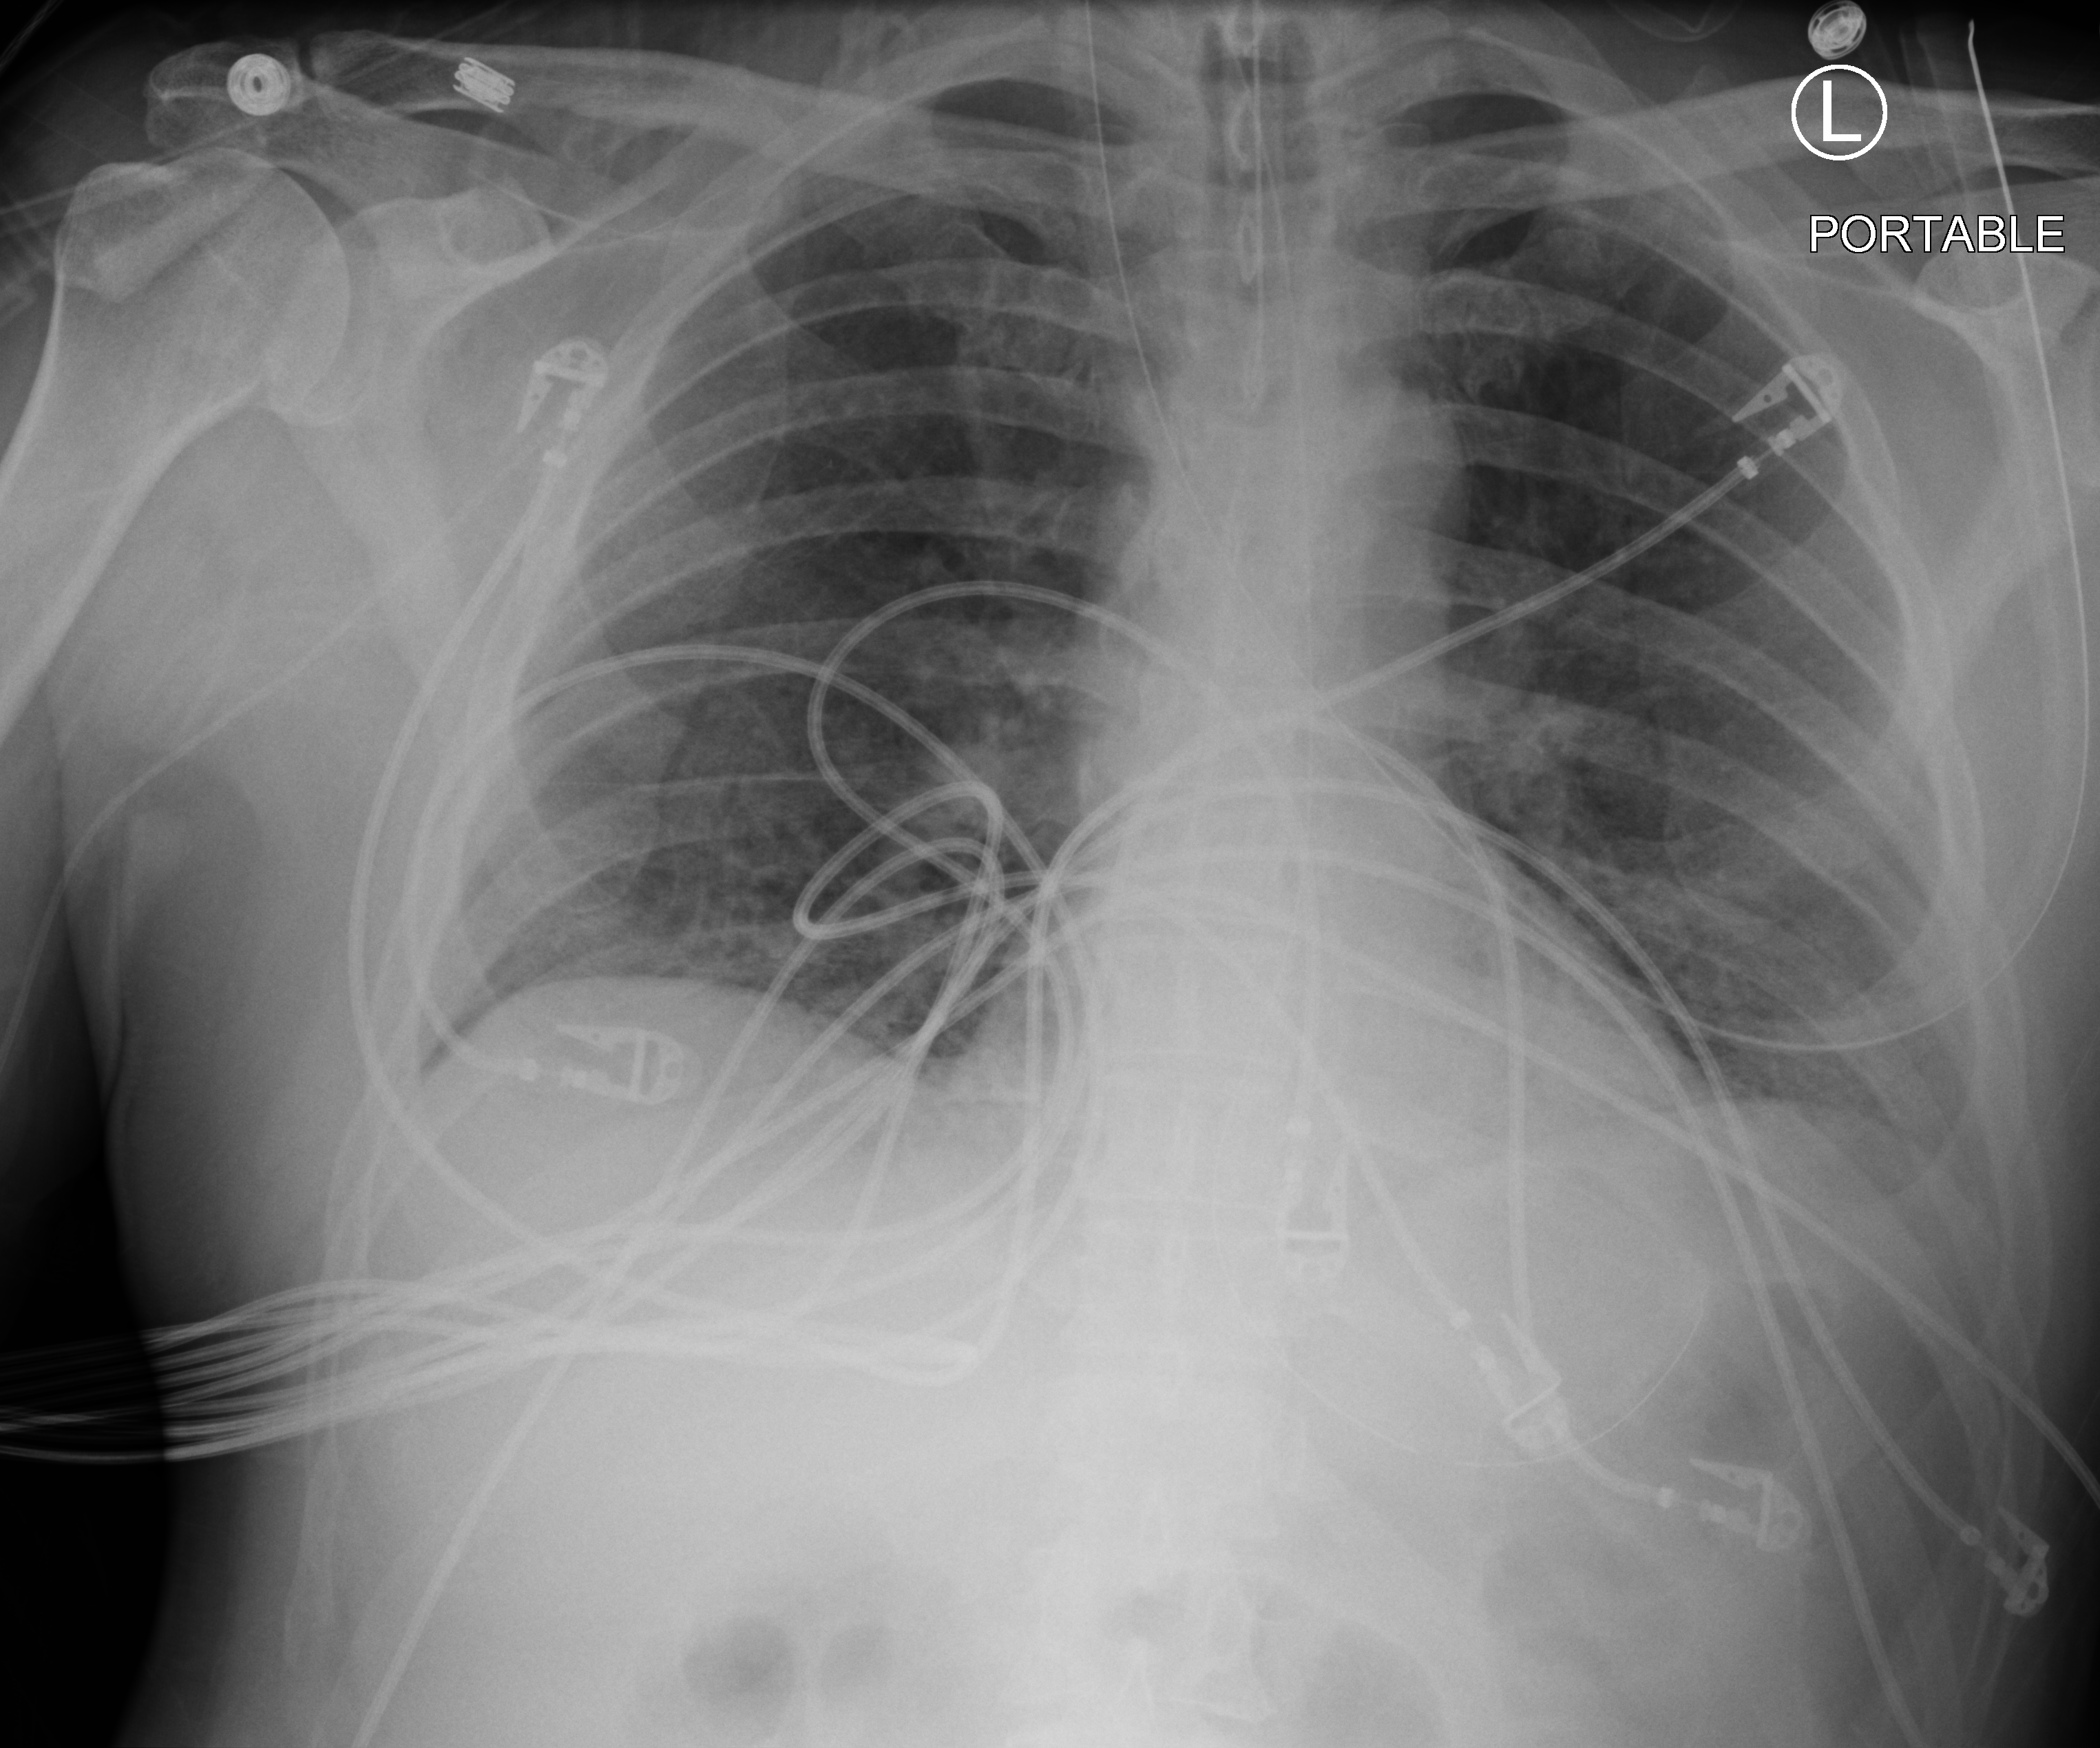
Chest X-ray (portable); anteroposterior (AP) projection. Male patient hospitalised with COVID-19, age 60–74 years.
Hospital-stay facts (about this admission, not read from this image; timing relative to this image not recorded):
- mechanically ventilated during this hospital stay: yes
- admitted to intensive care during this hospital stay: yes